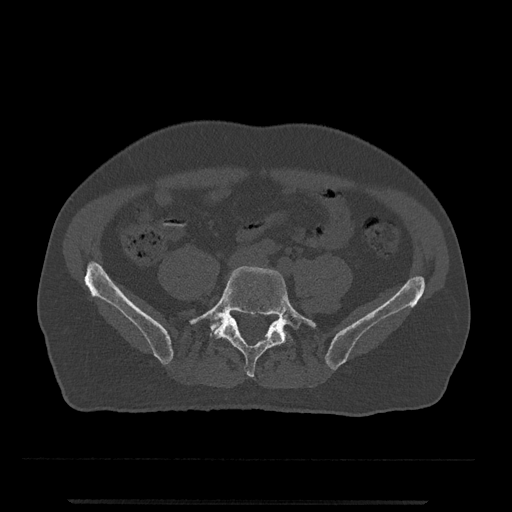
CT including the spine, one axial slice. Slice 72 of 797 in the series (ordered by position). Reconstruction kernel Br40s/3. Bone window (W 1800 / L 400 HU). 0.5 mm slice thickness. 512 × 512 image matrix, field of view 419 × 419 mm. Male patient, age 63 years. From the clinical record (not read from this slice): primary cancer: prostate.
Structures marked on this image (semi-automatic segmentation, software-assisted and operator-edited):
- L5 vertebra: bounding box <189,266,317,378> (left, top, right, bottom; pixels)